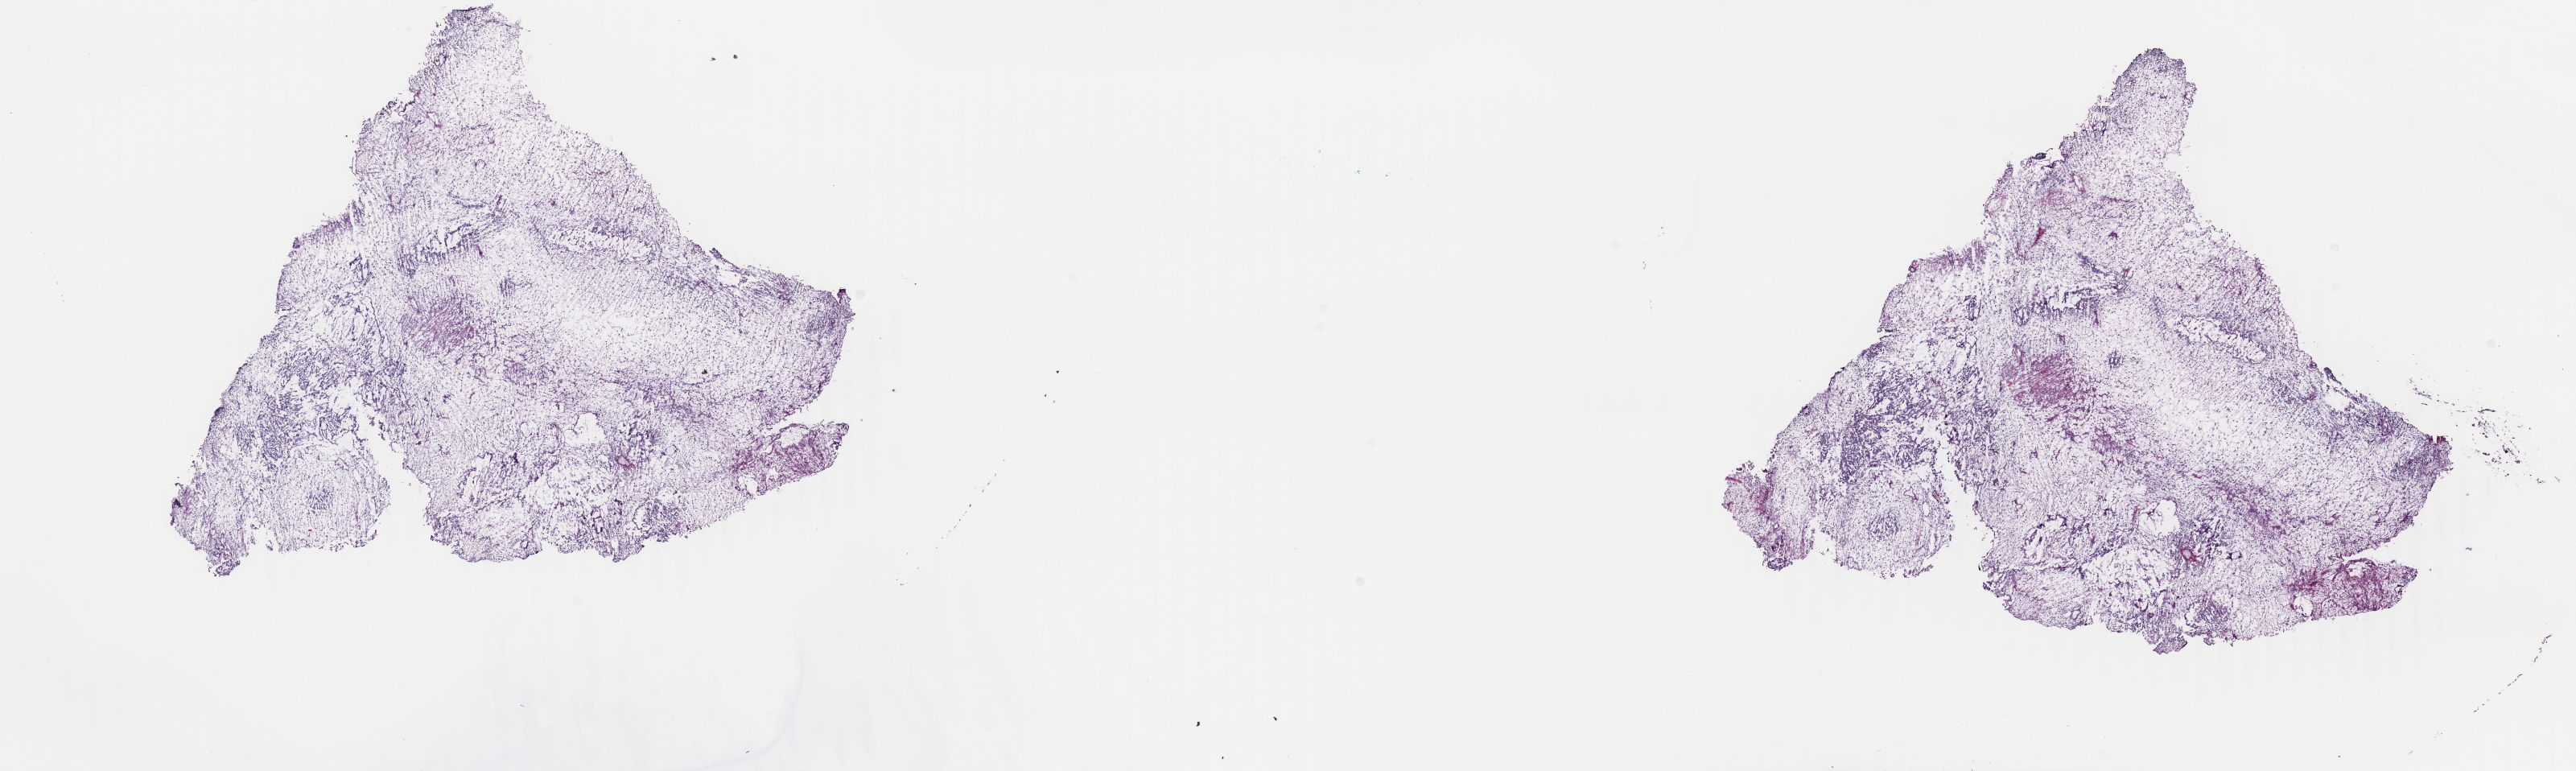
Whole-slide histology image, Hematoxylin and eosin (H&E) stained — low-resolution overview of the scanned area, about 25.5 x 7.6 mm (slide scanned at 40x), frozen section, testis, primary tumour sample. Male, age 28 years at initial diagnosis. Composition of this section per pathologist review: tumour cells 75%, tumour nuclei 75%, normal cells 0%, stromal cells 25%, necrosis 0%. Inflammatory infiltration, as recorded: lymphocyte infiltration 3%, monocyte infiltration 1%, neutrophil infiltration 2%.
AJCC pathologic stage: IS. Diagnosis: Mixed germ cell tumor. TNM: T1 N0 M0. Laterality: left.